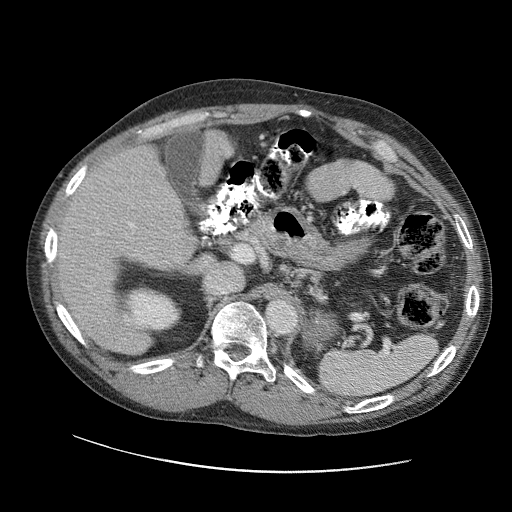
Contrast-enhanced abdominal CT (liver protocol), one axial slice; slice 63 of 109 in the series (ordered by position); reconstruction kernel STANDARD; 120 kVp; soft-tissue window (W 400 / L 40 HU); 2.5 mm slice thickness; 512 × 512 image matrix, field of view 400 × 400 mm. From the clinical record (not read from this slice): diagnosis: hepatocellular carcinoma (patient treated with transarterial chemoembolisation; whether this scan precedes or follows treatment is not stated here); TNM stage (as recorded): Stage-IIIC; Child-Pugh class: B; tumour nodularity: uninodular.
Outlined on this slice (semi-automatic segmentation, software-assisted and operator-edited):
- liver parenchyma outside the tumour (the mass and vessels are separate outlines, so this box may not span the whole liver): bounding box <54,144,194,316> (left, top, right, bottom; pixels)
- liver vessels: <90,190,160,288>